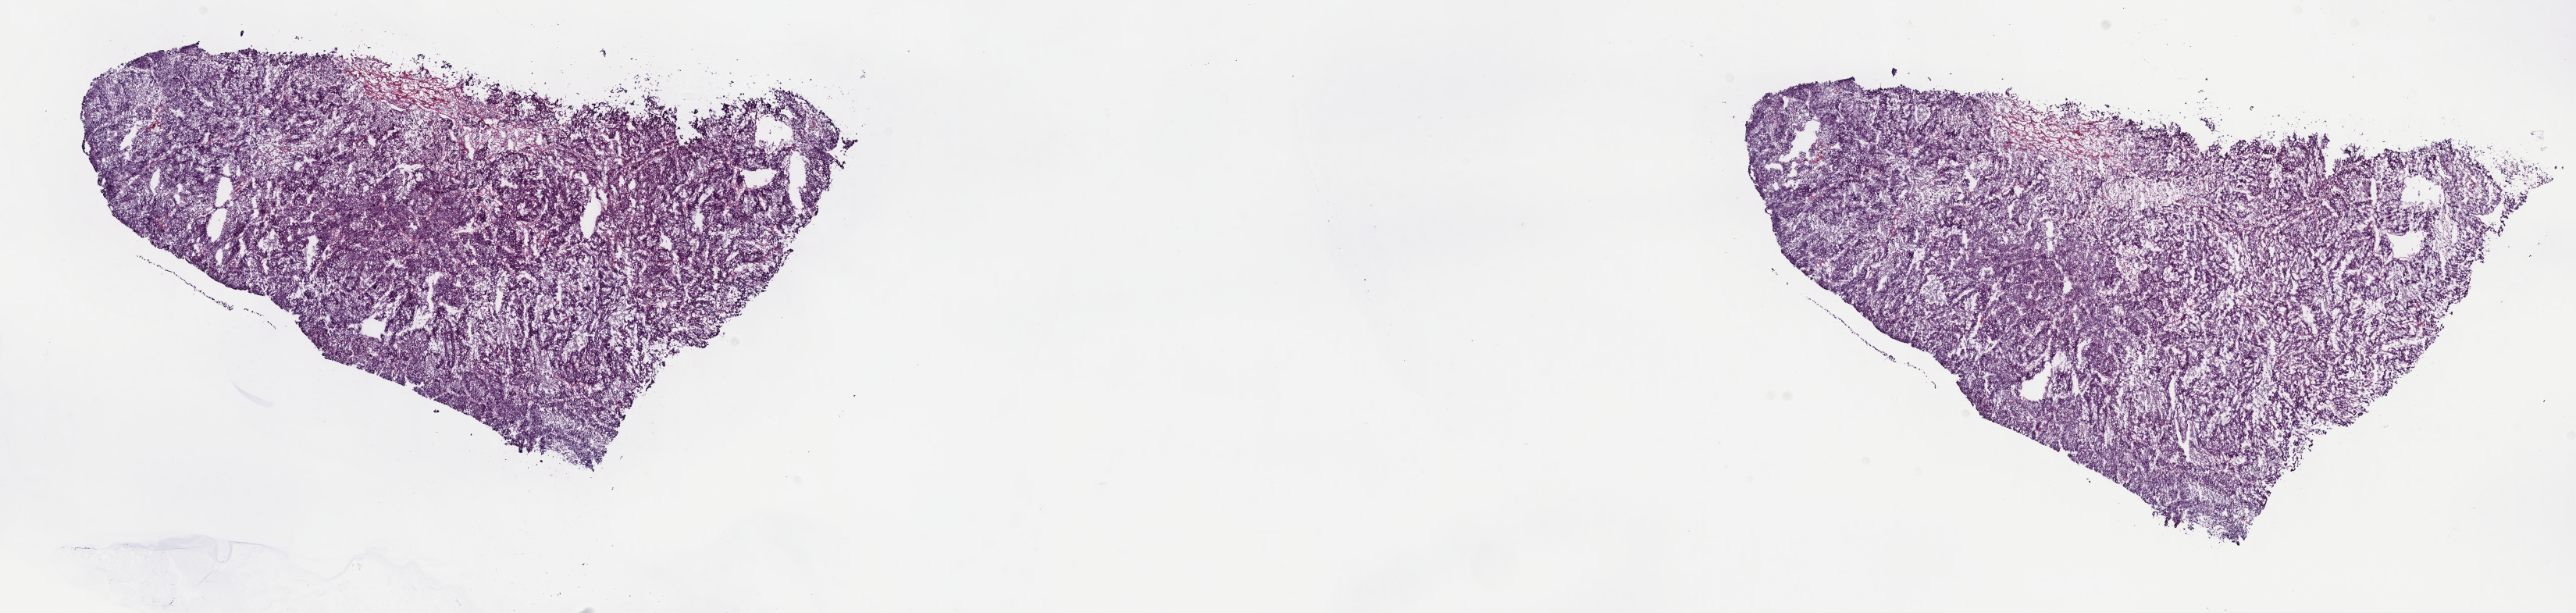
Digitized Hematoxylin and eosin (H&E) stained tissue section (whole slide), whole scanned area (about 26.7 x 6.3 mm, slide scanned at 40x) shown as a low-resolution overview; frozen section from the top of the tissue portion; primary tumour sample from the liver. Patient: female, age at initial diagnosis 63 years. Histologic grade: G4 (undifferentiated). Slide review estimates, as recorded: tumour cells 100%, tumour nuclei 90%, normal cells 0%, stromal cells 0%, necrosis 0%. Inflammatory infiltration, as recorded: lymphocyte infiltration 0%, monocyte infiltration 0%, neutrophil infiltration 0%.
- diagnosis: Hepatocellular carcinoma, NOS
- AJCC pathologic stage: I (7th edition)